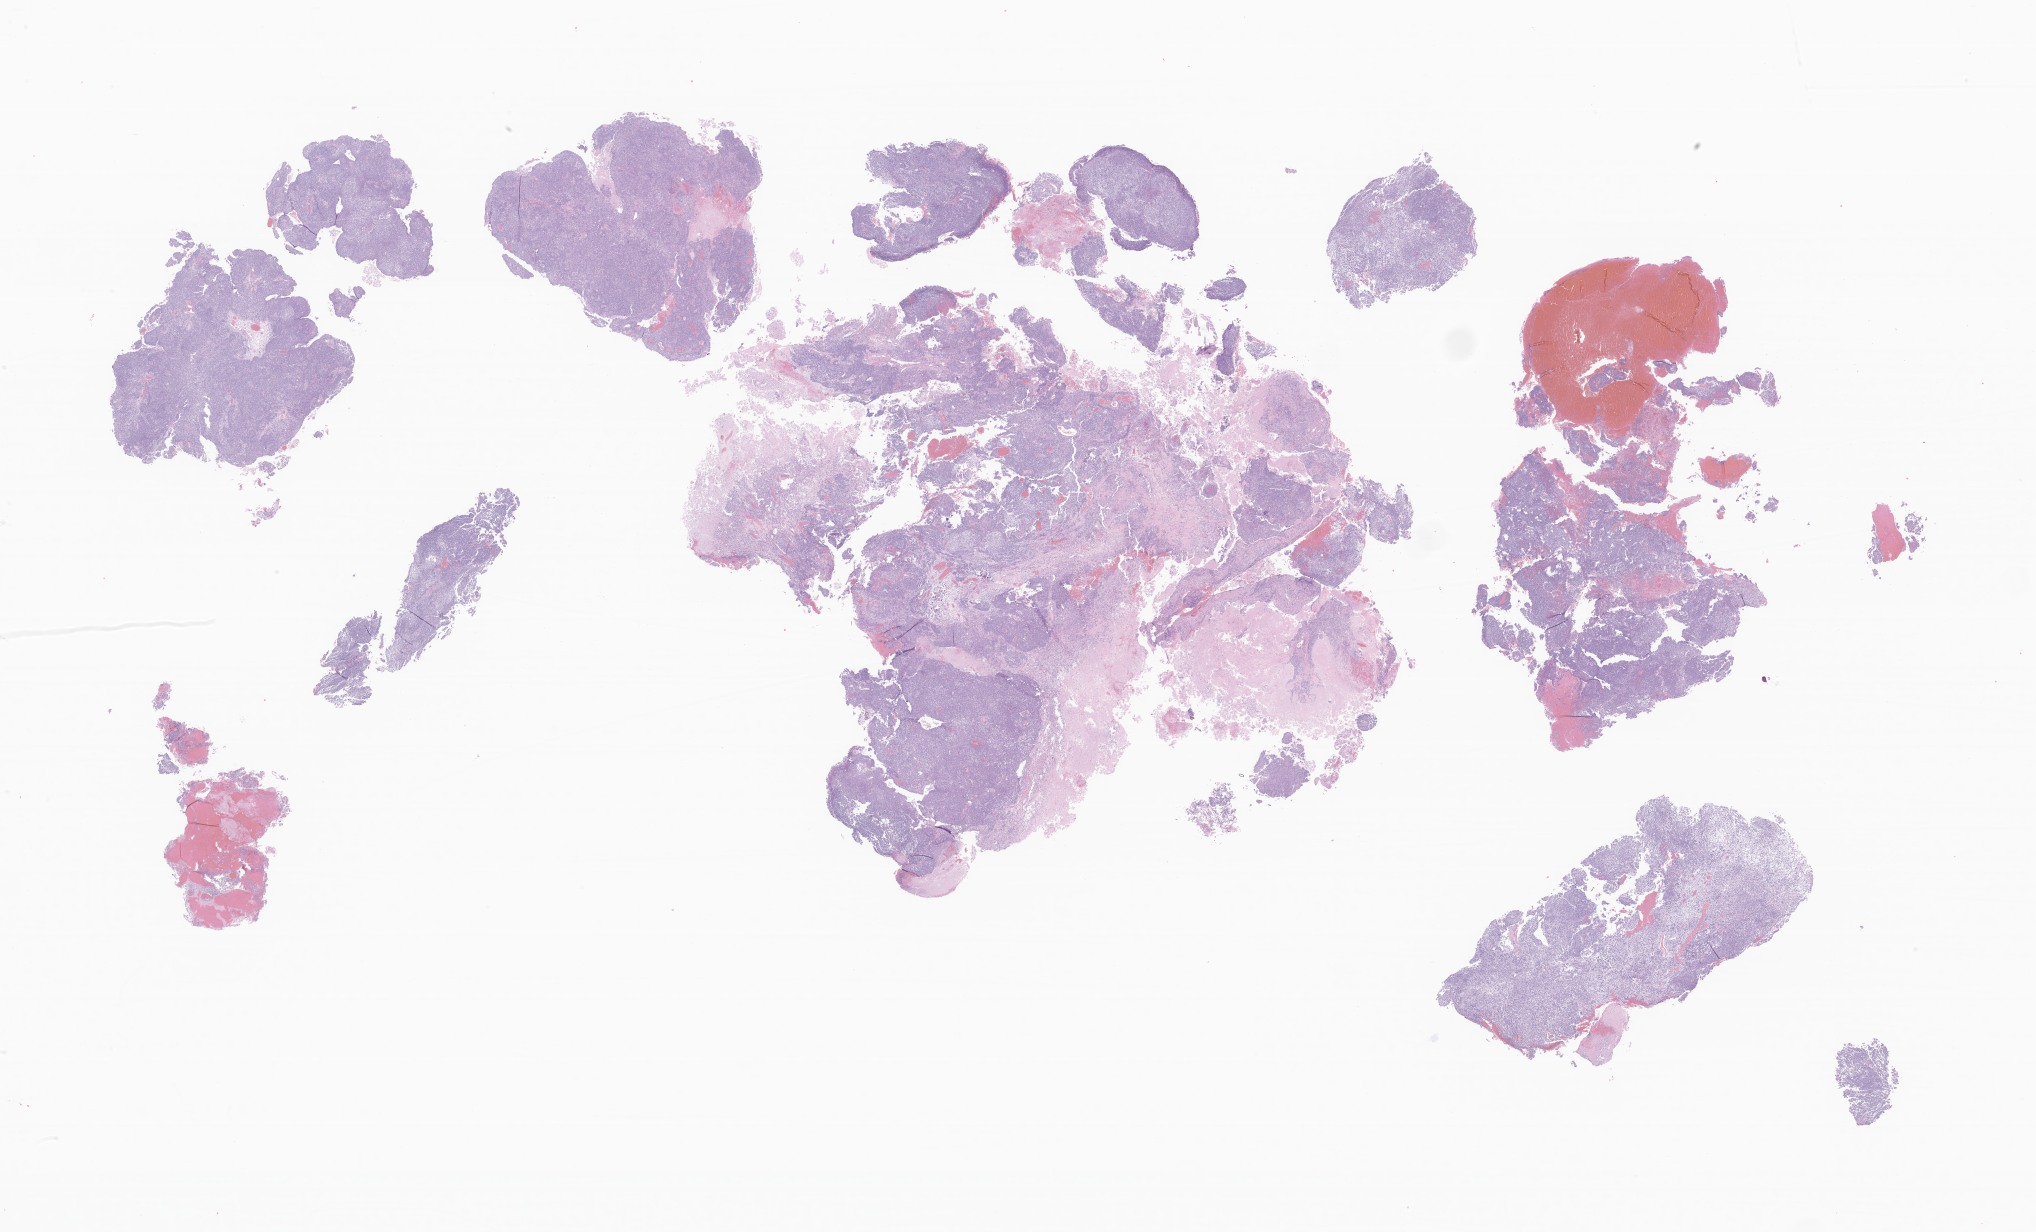
Digitized H&E-stained section of tumor tissue from the brain, whole scanned area (about 34.3 x 20.8 mm) shown as a low-resolution overview. Formalin-fixed, paraffin-embedded (FFPE) tissue. Female patient, age 306 days.
* diagnosis: Rhabdoid tumor, NOS